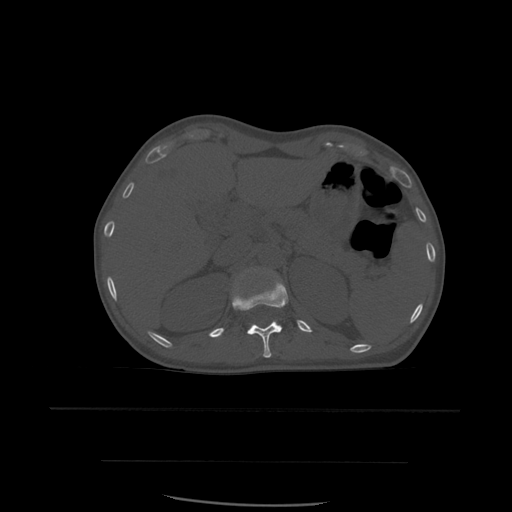
CT including the spine, one axial slice; position 269 of 574 along the scan axis; bone window (W 1800 / L 400 HU); 512 × 512 image matrix, field of view 392 × 392 mm. Patient age 48 years. Case-level facts recorded for this patient, not image findings: primary cancer: lung; vertebrae with lytic lesions (as recorded): T11.
Structures marked on this image (semi-automatic segmentation, software-assisted and operator-edited):
- T12 vertebra: bounding box [x1, y1, x2, y2] px = [232, 277, 289, 358]